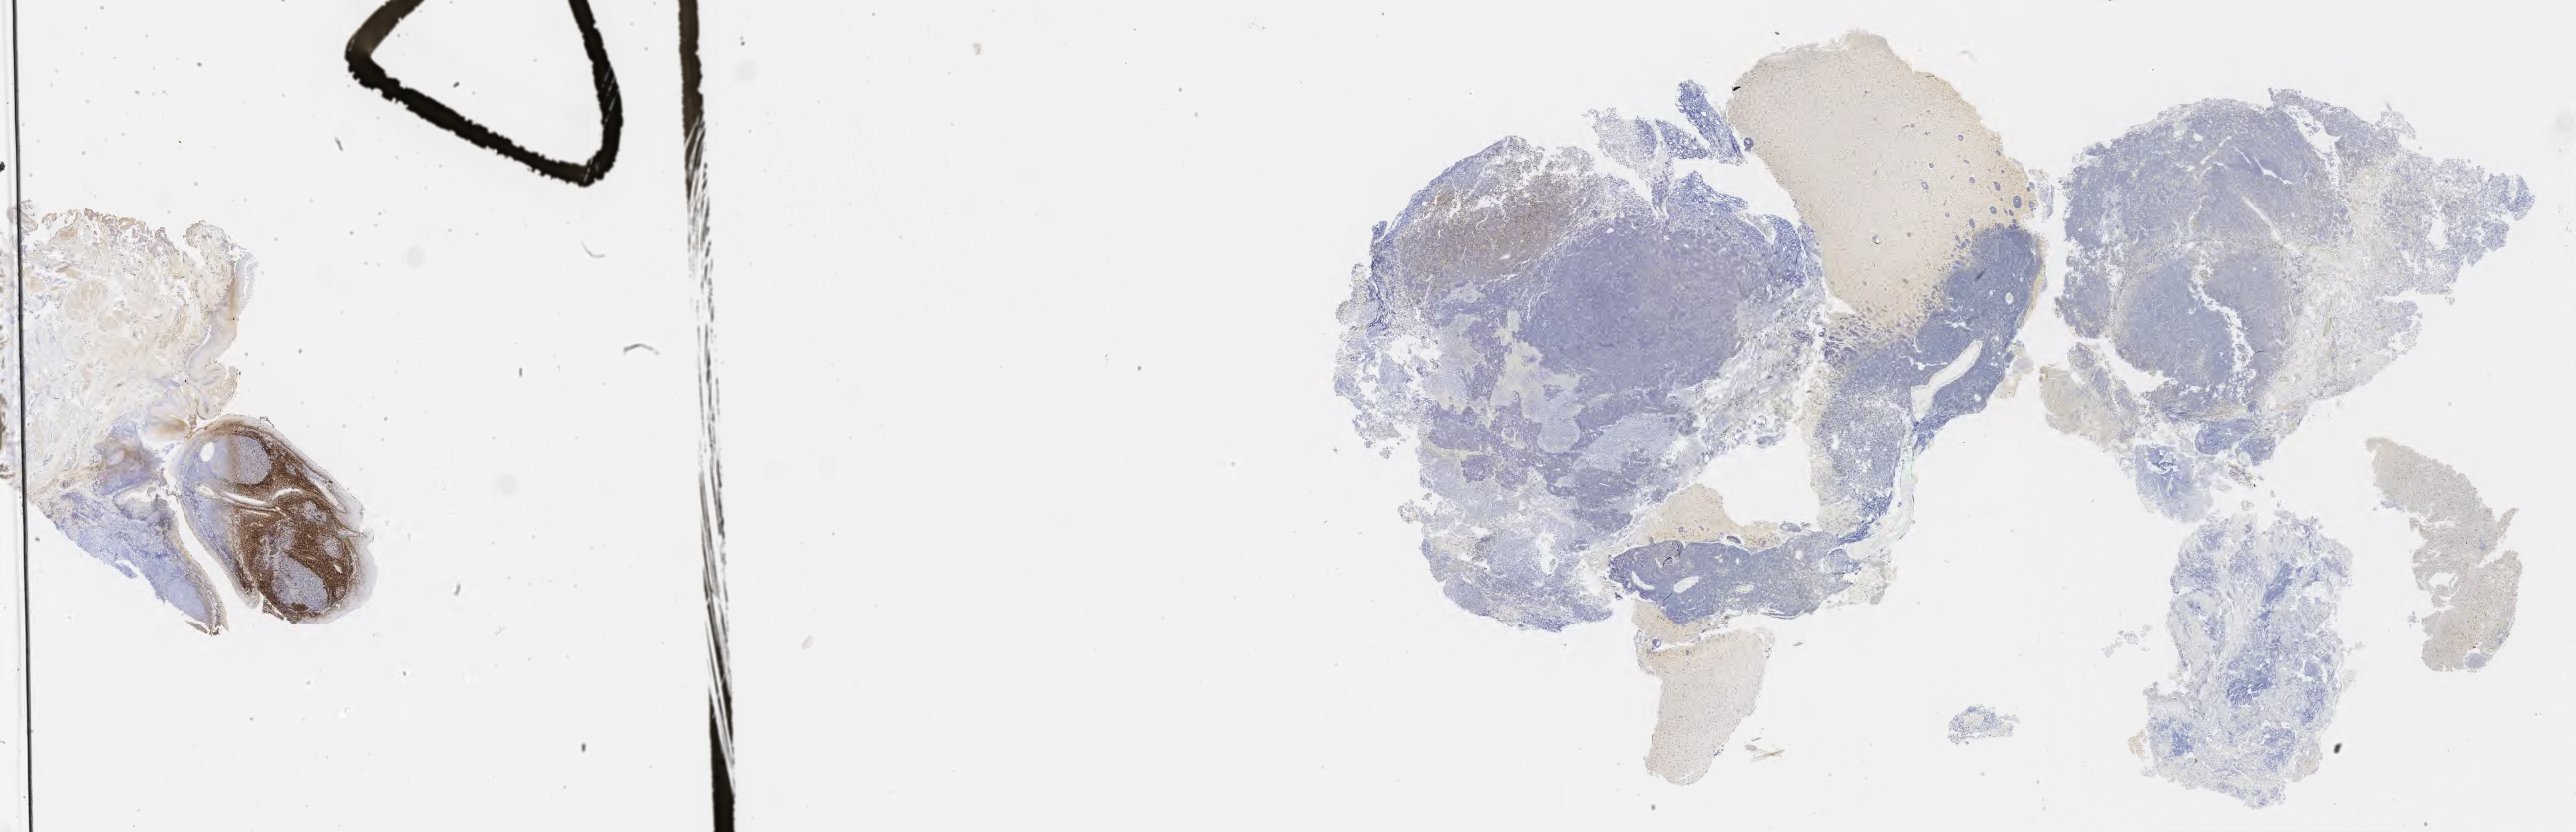
IHC for BCL2, whole-slide image — whole scanned area (about 41.8 x 13.5 mm) shown as a low-resolution overview; specimen: tumor tissue. Patient female; age 73 years.
- diagnosis: Burkitt lymphoma, NOS